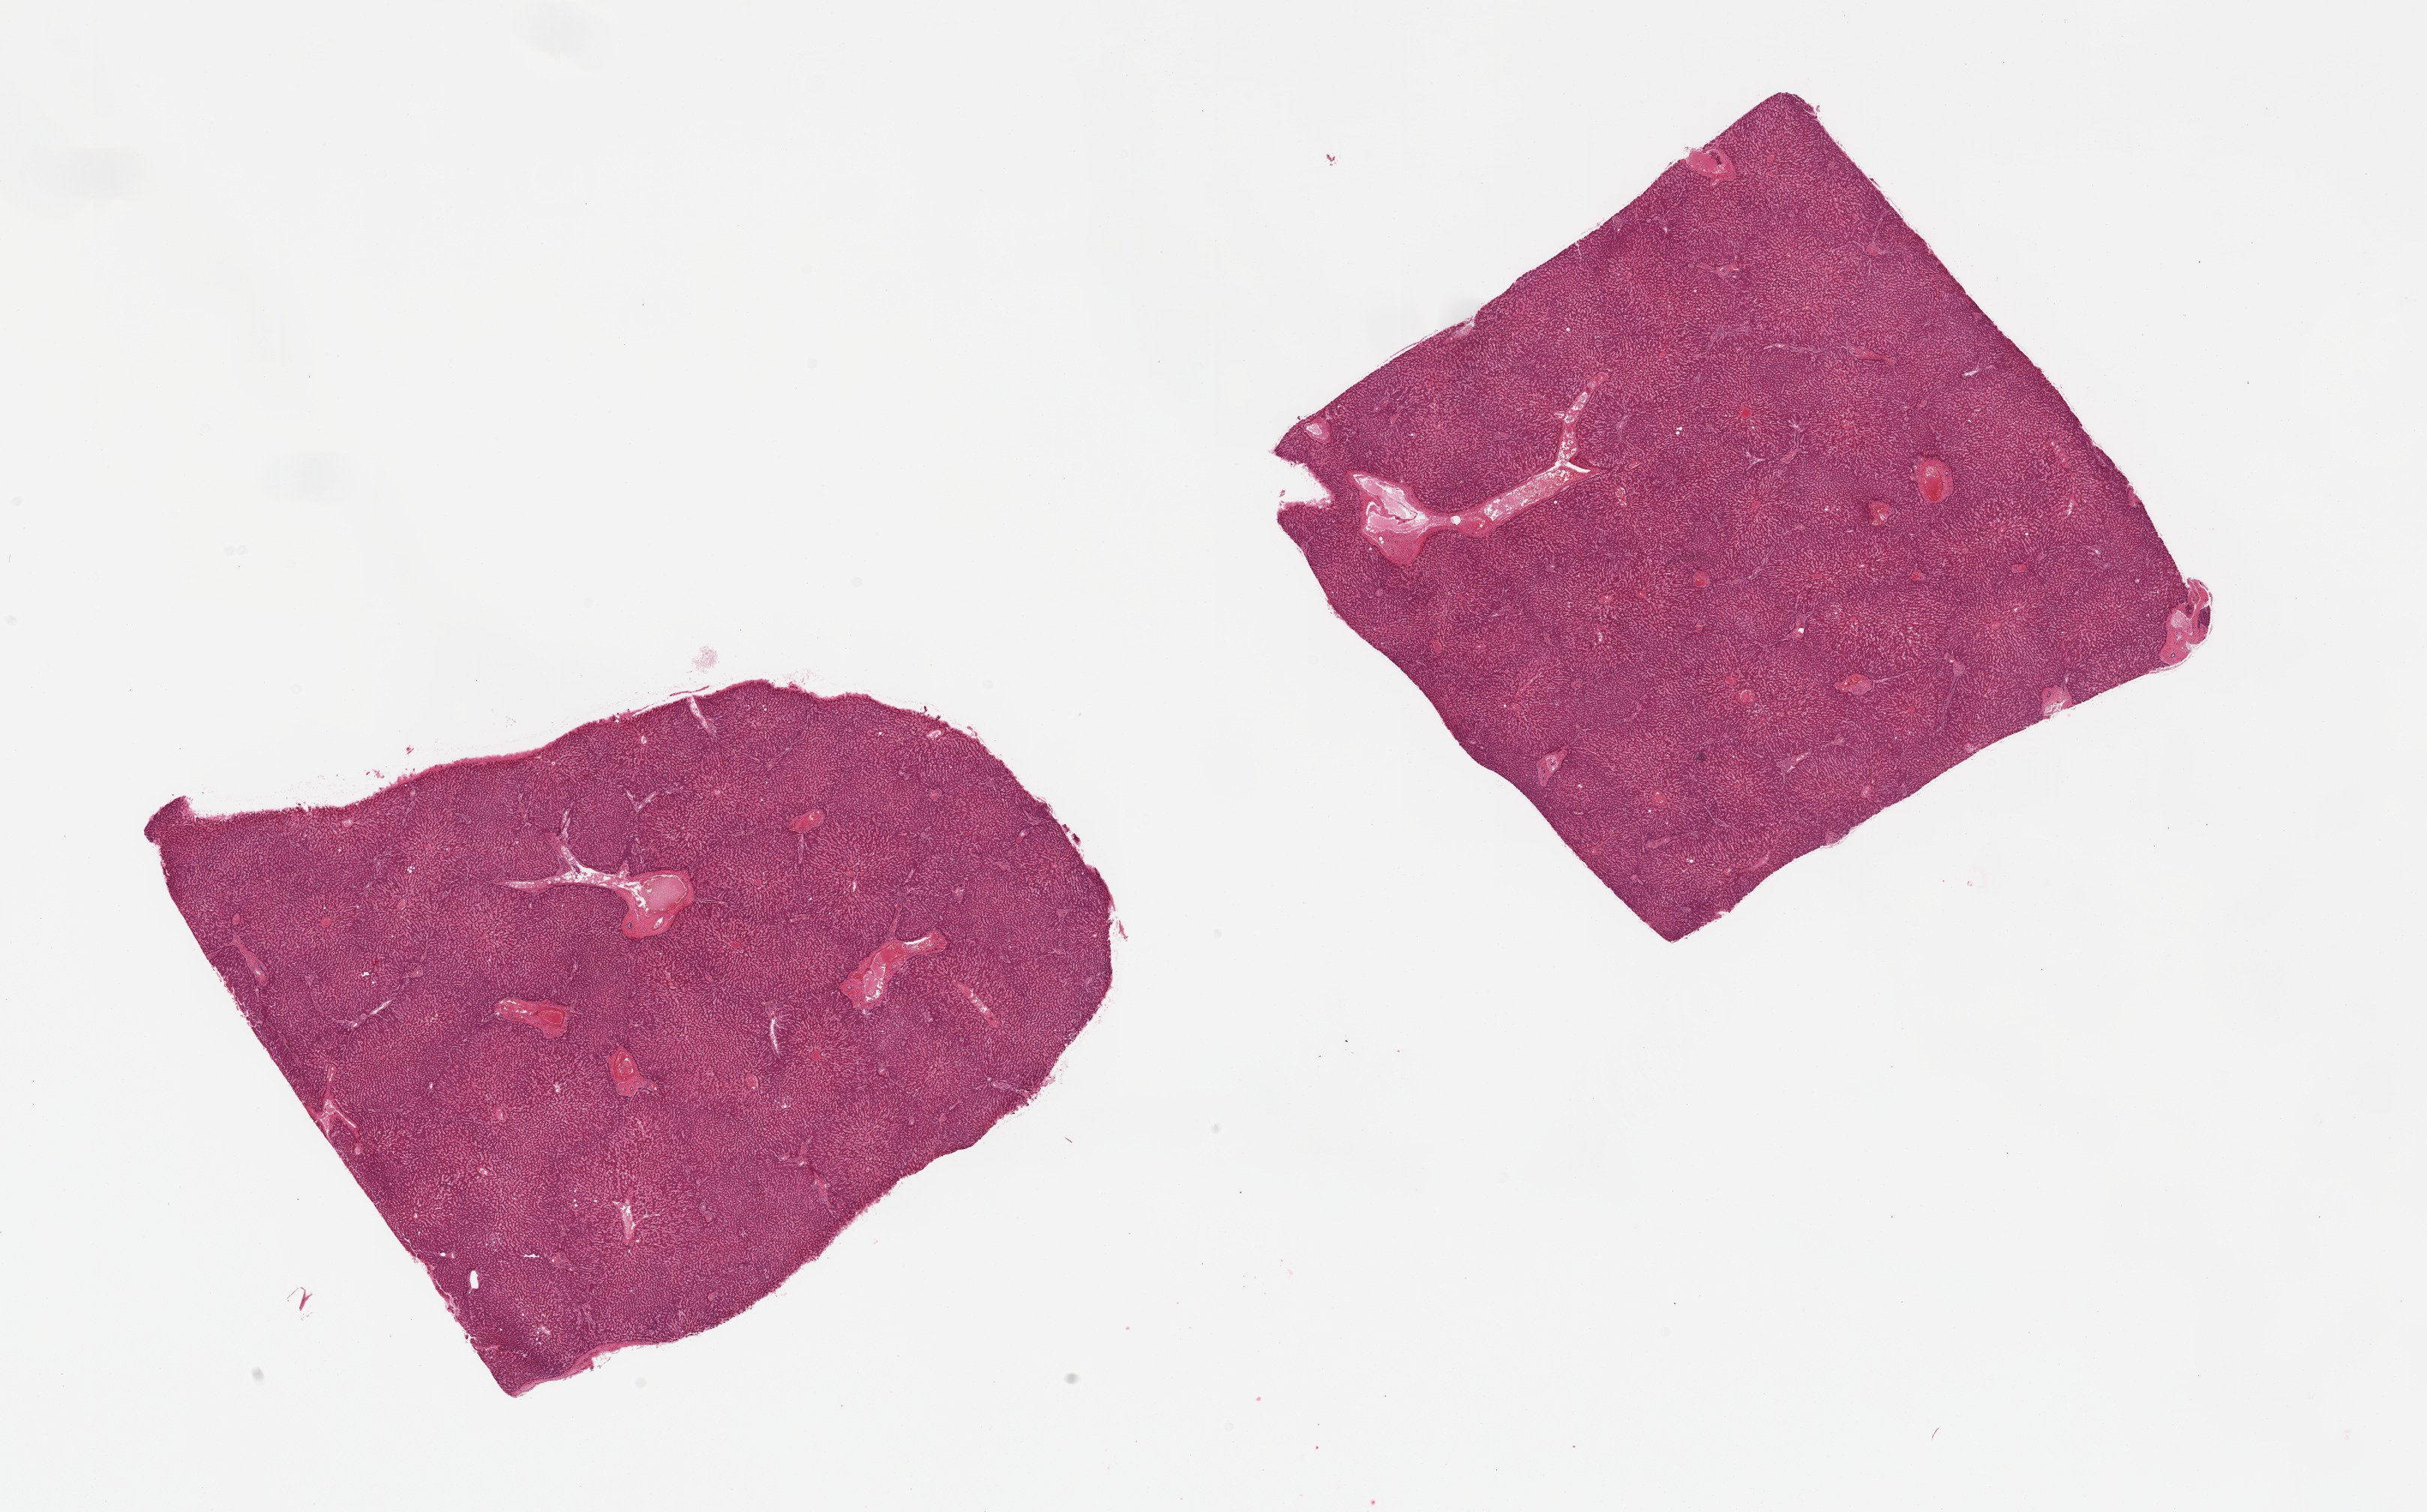
Hematoxylin and eosin (H&E) whole-slide image, brightfield — low-resolution overview of the scanned area, about 25.6 x 15.9 mm (slide scanned at 20x); PAXgene-fixed paraffin-embedded (PFPE) section; section of liver (target tissue); tissue donor sample. Male donor.
Review note (as recorded): 2 pieces; congestion.